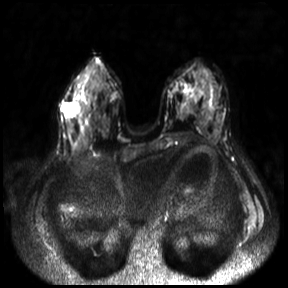
Breast MRI, one axial slice; position 12 of 30 along the scan axis; diffusion-weighted series; image 2 of 4 stored at this slice position (different b-values; order by instance number); 3 T; 4 mm slice thickness; 288 × 288 image matrix, field of view 360 × 360 mm. Female patient.
Structures marked on this image (manually delineated by an expert):
- tumour on diffusion-weighted imaging: bounding box <62,102,80,116> (left, top, right, bottom; pixels)